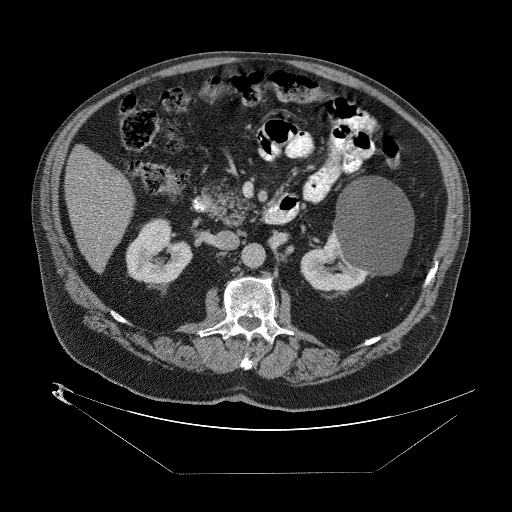
Contrast-enhanced abdominal CT (liver protocol), one axial slice. Position 20 of 89 along the scan axis. Reconstruction kernel STANDARD. 140 kVp. One of 2 acquisitions stored at this slice position. Soft-tissue window (W 400 / L 40 HU). 2.5 mm slice thickness. 512 × 512 image matrix, field of view 480 × 480 mm. From the clinical record (not read from this slice): diagnosis: hepatocellular carcinoma (patient treated with transarterial chemoembolisation; whether this scan precedes or follows treatment is not stated here); TNM stage (as recorded): Stage-II; Child-Pugh class: B; tumour differentiation: moderately differentiated.
Annotated regions visible in this slice (semi-automatically segmented with operator editing):
- abdominal aorta: bounding box (x1, y1, x2, y2) in pixels: (244, 244, 265, 266)
- liver parenchyma outside the tumour (the mass and vessels are separate outlines, so this box may not span the whole liver): (62, 144, 134, 268)
- liver vessels: (93, 176, 125, 236)